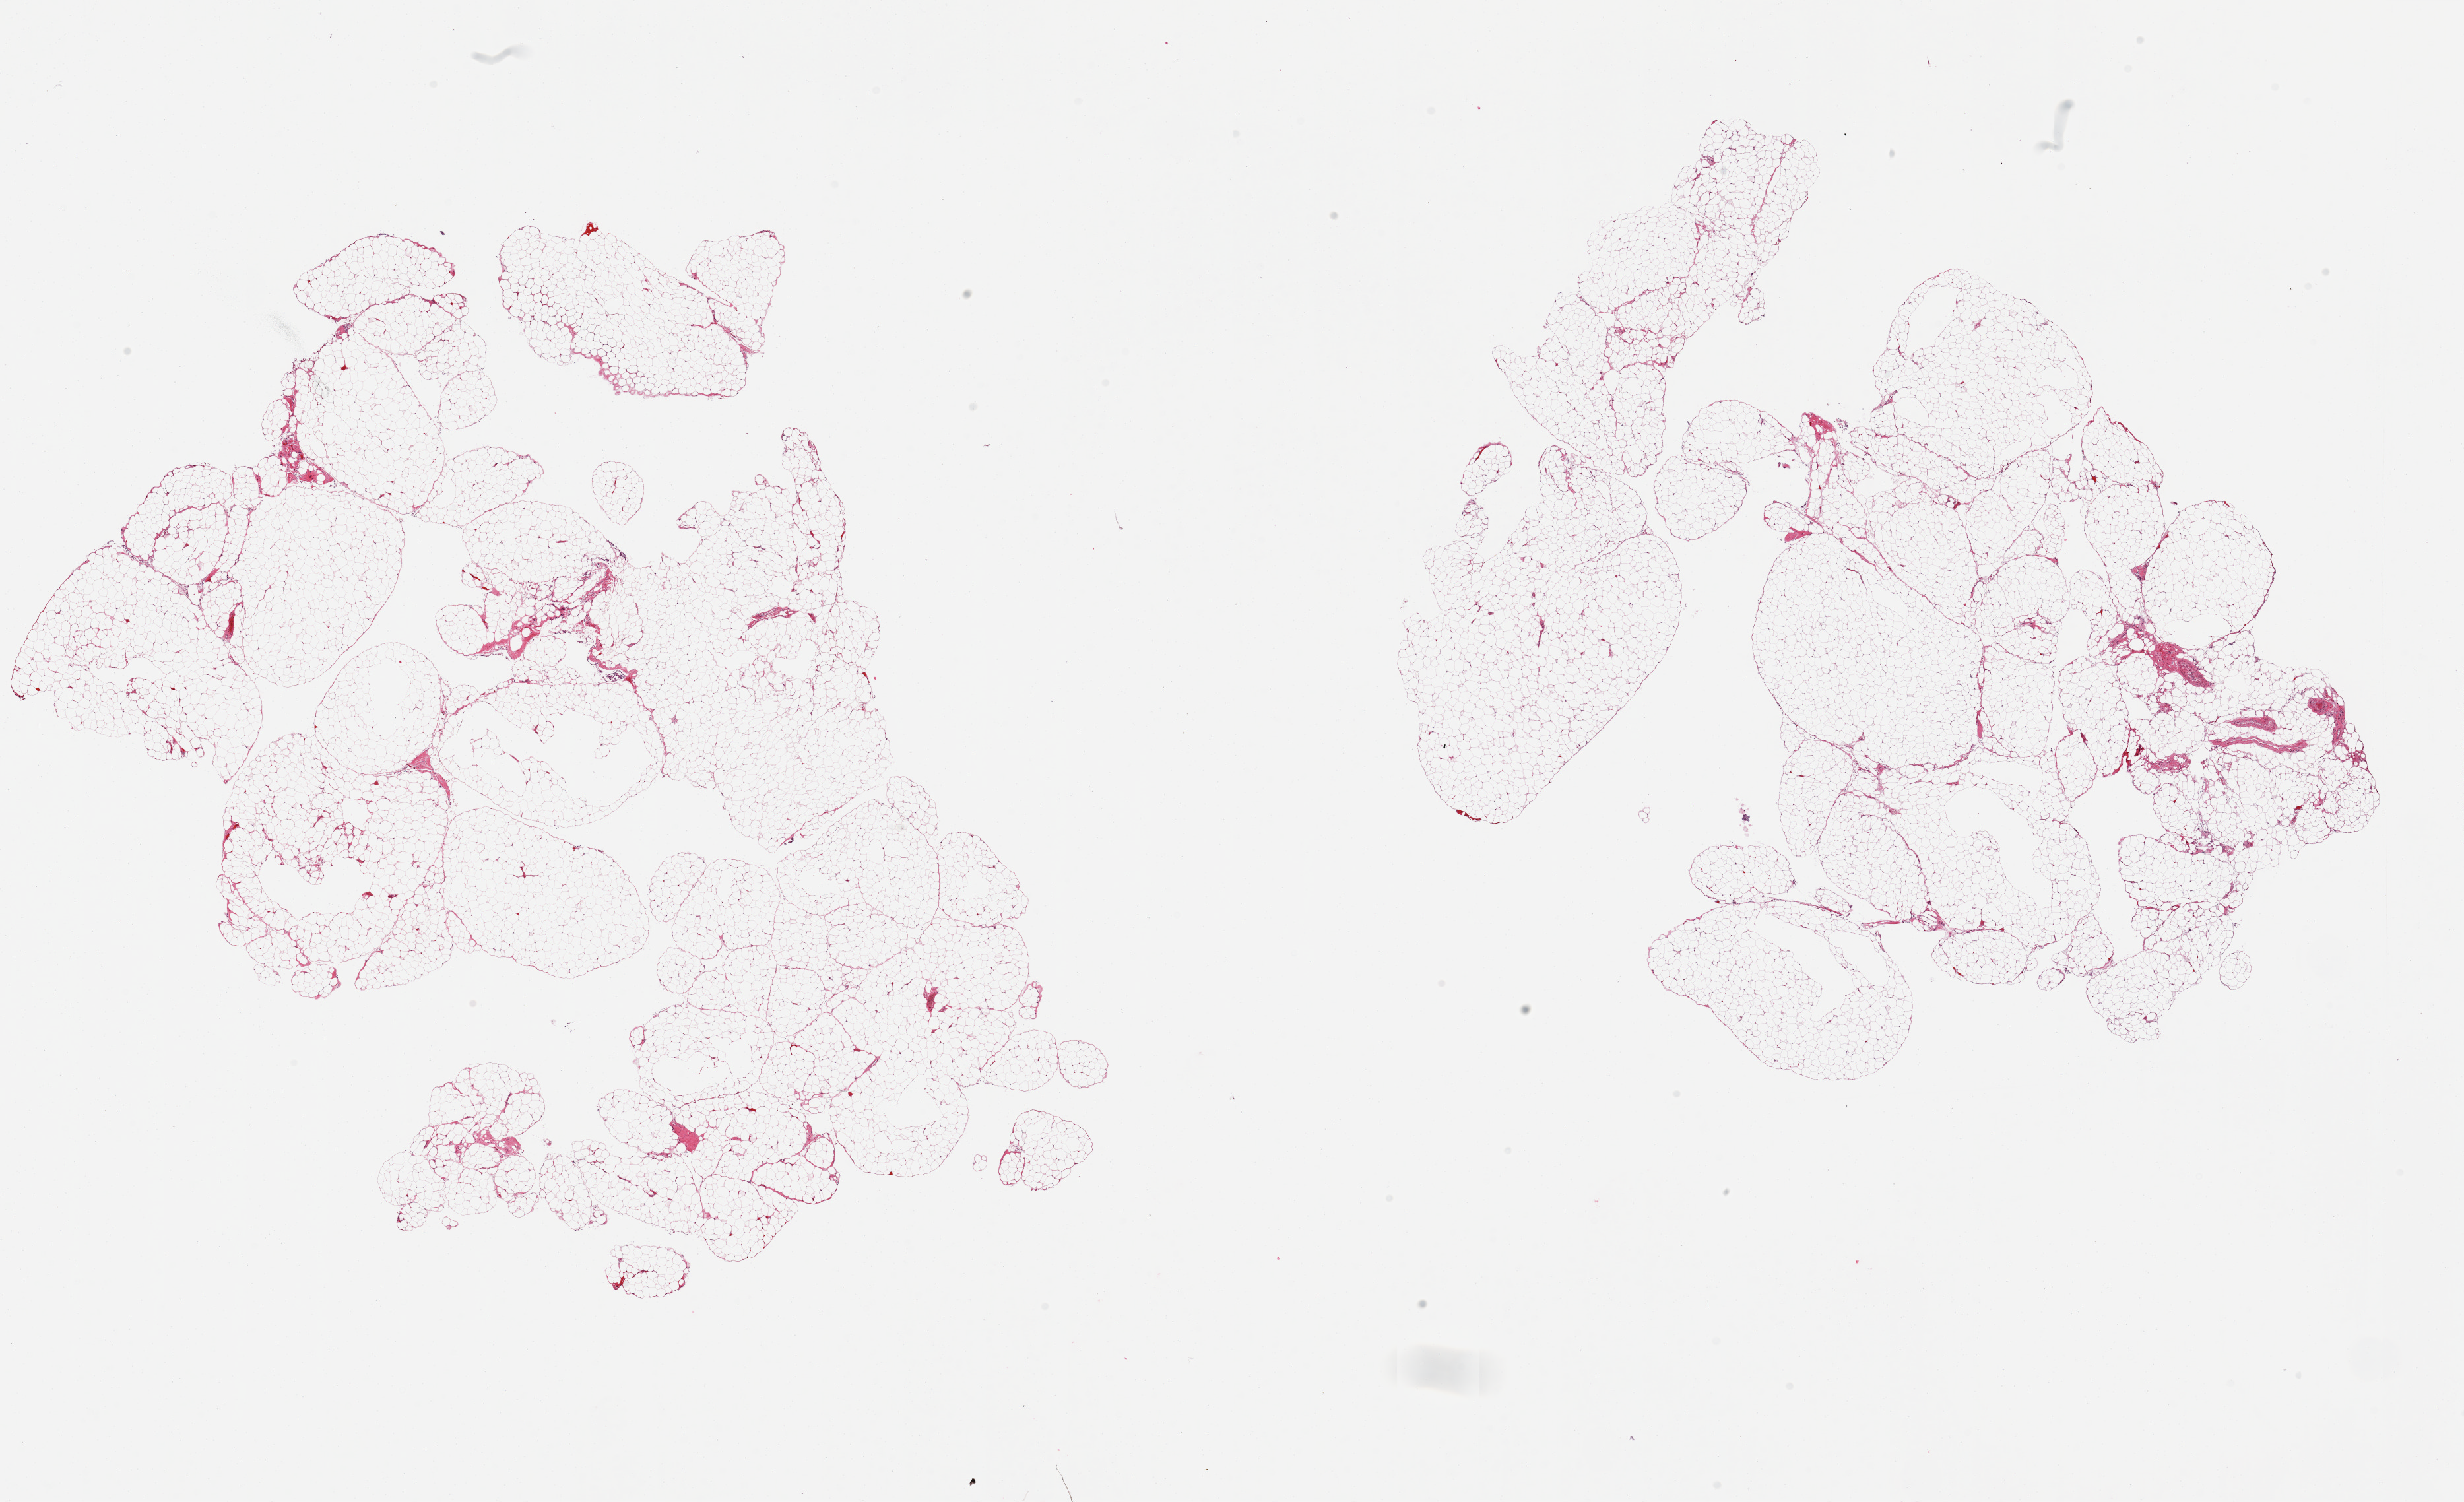
Digitized hematoxylin and eosin (H&E)-stained section, brightfield, shown as a low-resolution overview of the whole scanned area (about 29.5 x 18.0 mm, from a 20x scan), PAXgene-fixed, paraffin-embedded tissue, sampled site (target tissue): omentum, donor tissue sample.
Review note (as recorded): 2 pieces; minimal fibrovascular component.